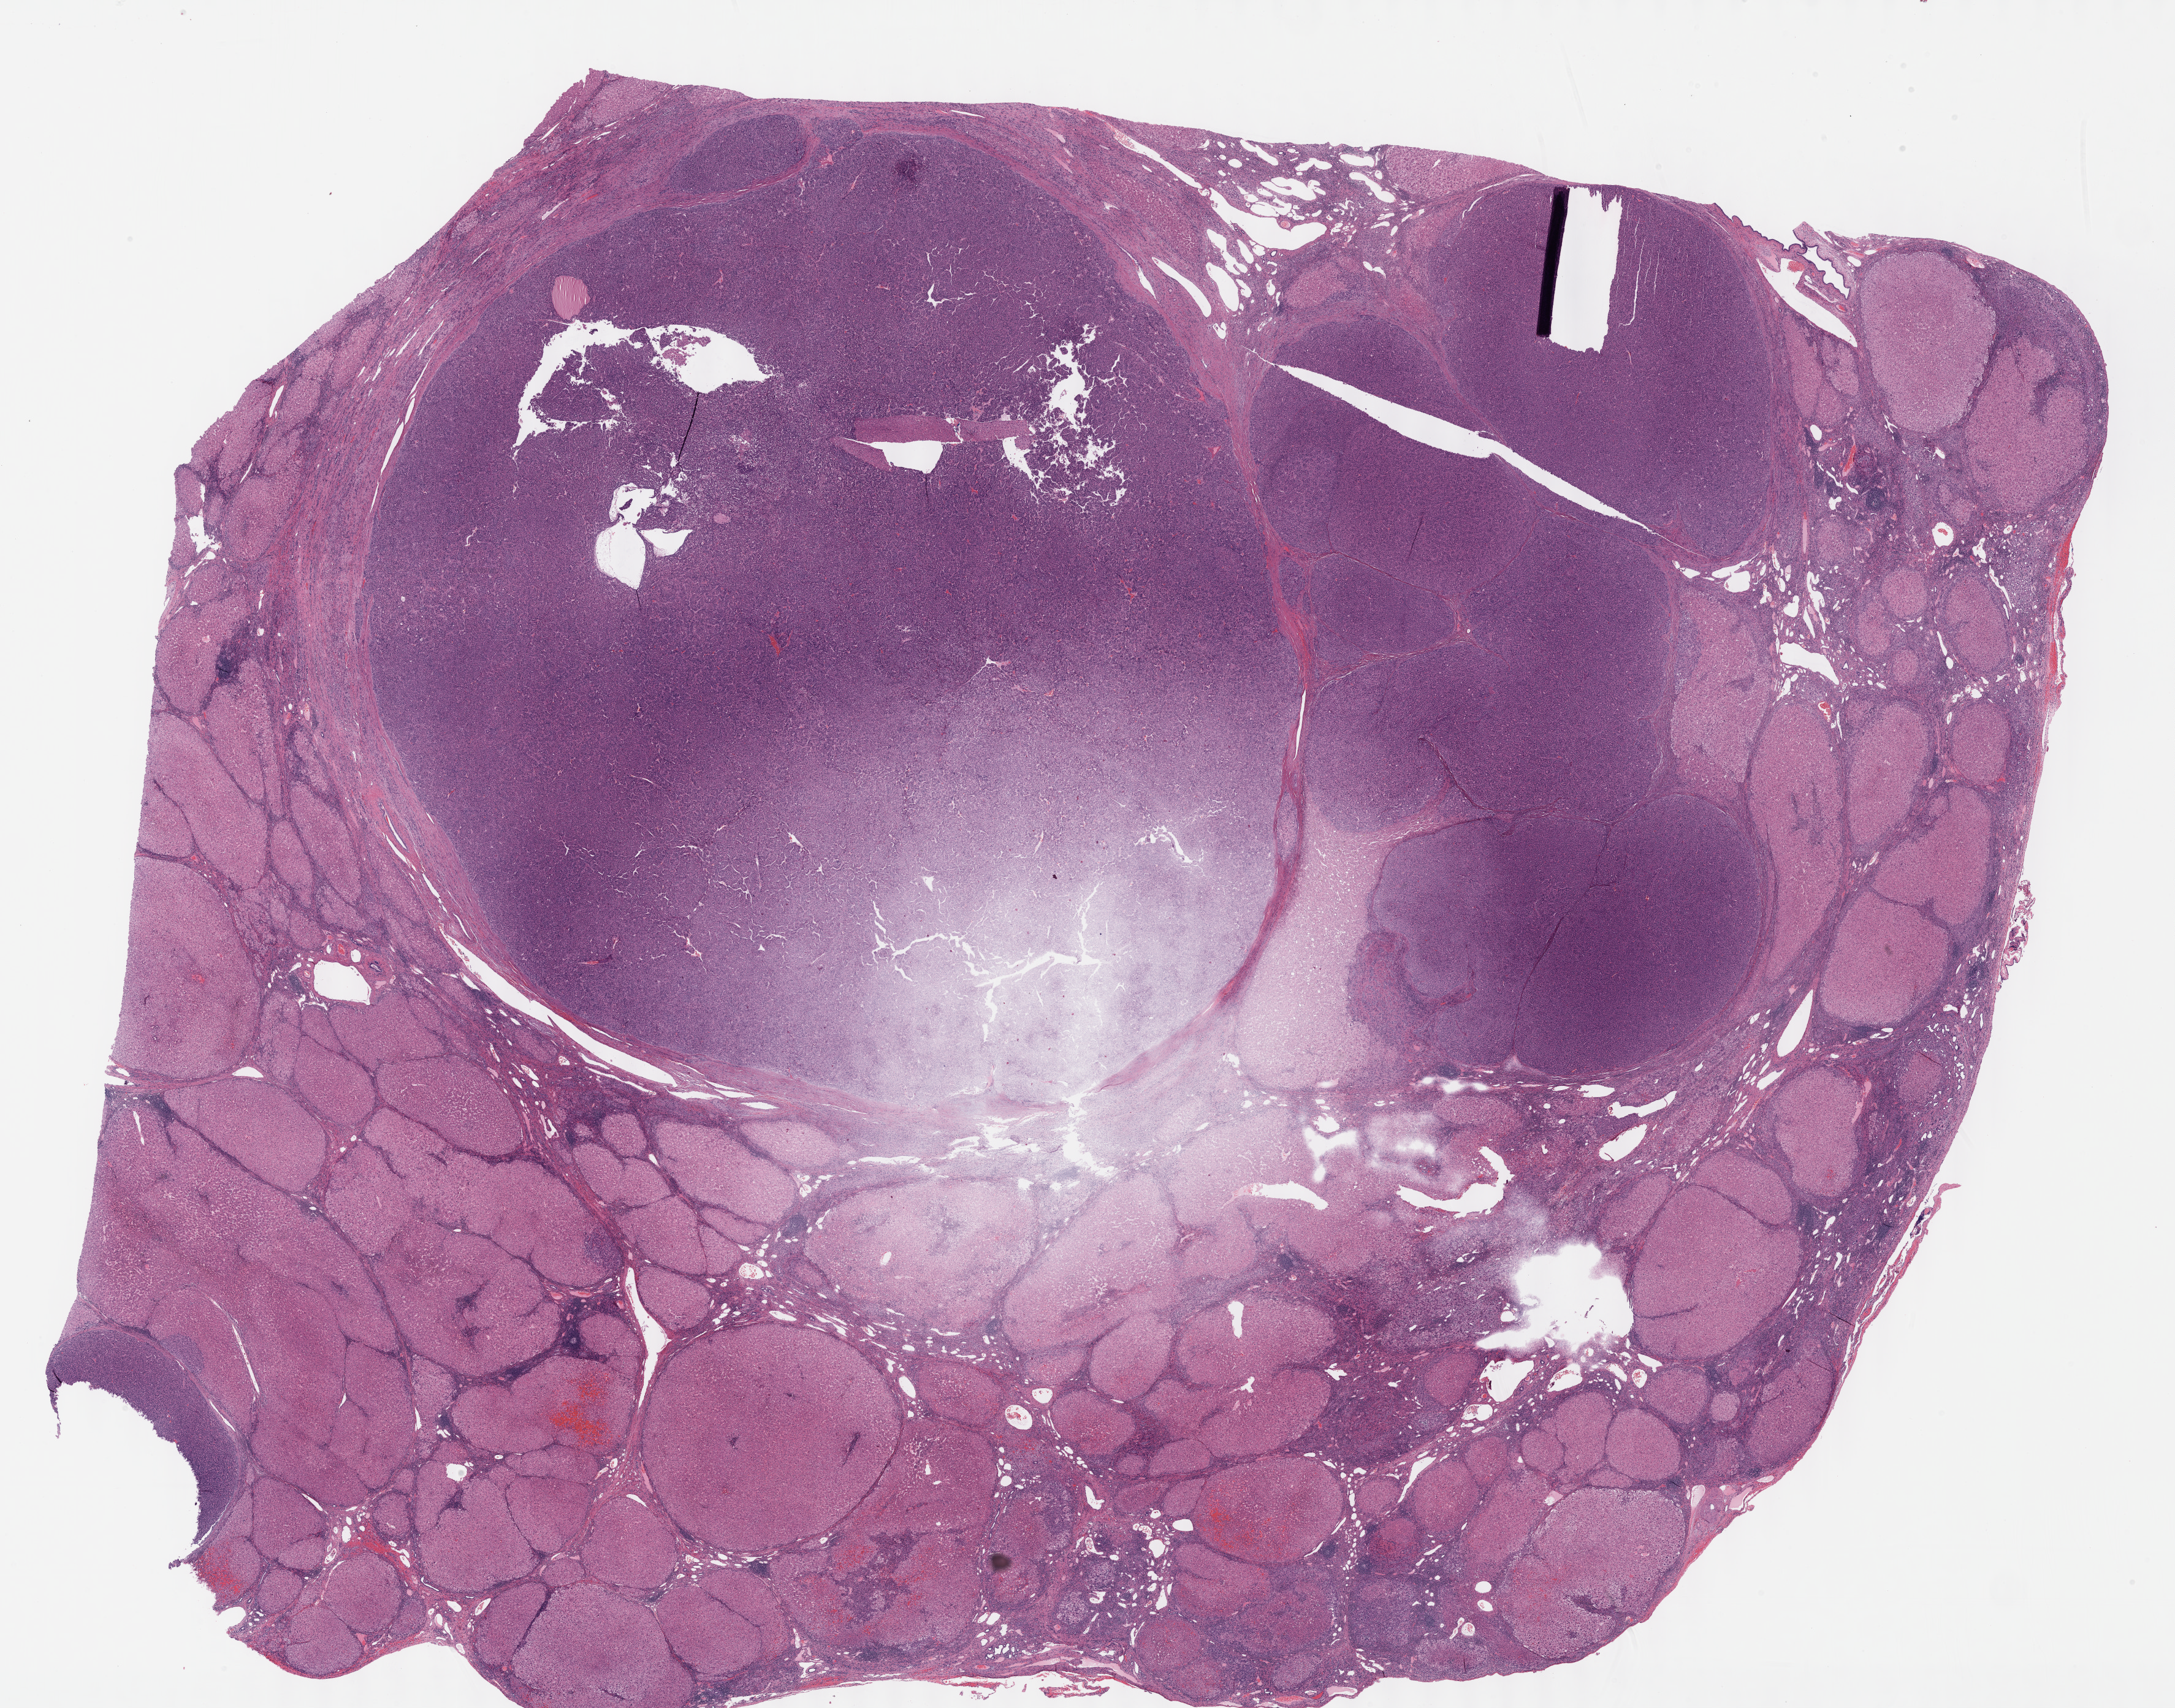
Whole-slide histology image, H&E — whole scanned area (about 28.7 x 22.5 mm, from a 40x scan) shown as a low-resolution overview, formalin-fixed paraffin-embedded (FFPE) diagnostic section, liver, primary tumour sample. Male patient; age at initial diagnosis 44 years. Histologic grade: G2 (moderately differentiated).
TNM: T2 N0 M0. AJCC pathologic stage: II (7th edition). Histologic diagnosis: Hepatocellular carcinoma, NOS.